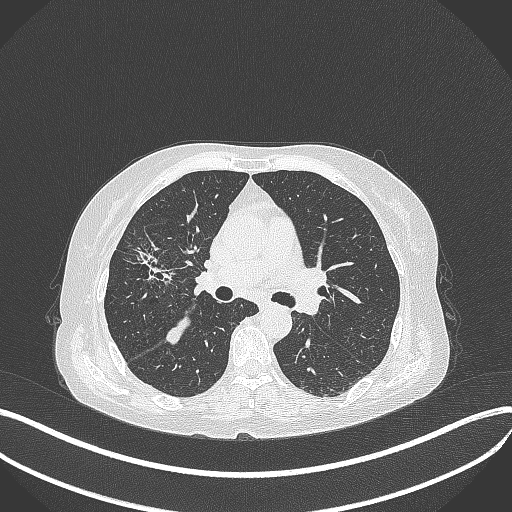
Chest CT, one axial slice. Slice 235 of 429 in the series (ordered by position). Reconstruction kernel B70f. Lung window (W 1500 / L -600 HU). 1 mm slice thickness. 512 × 512 image matrix. Female patient, age 69 years. From the clinical record (not read from this slice): clinical TNM (as recorded): T1b N3 M0.
Structures marked on this image (rectangle marked by the reading radiologist):
- lung tumour (recorded histology: small cell carcinoma): bounding box <119,237,178,289> (left, top, right, bottom; pixels)